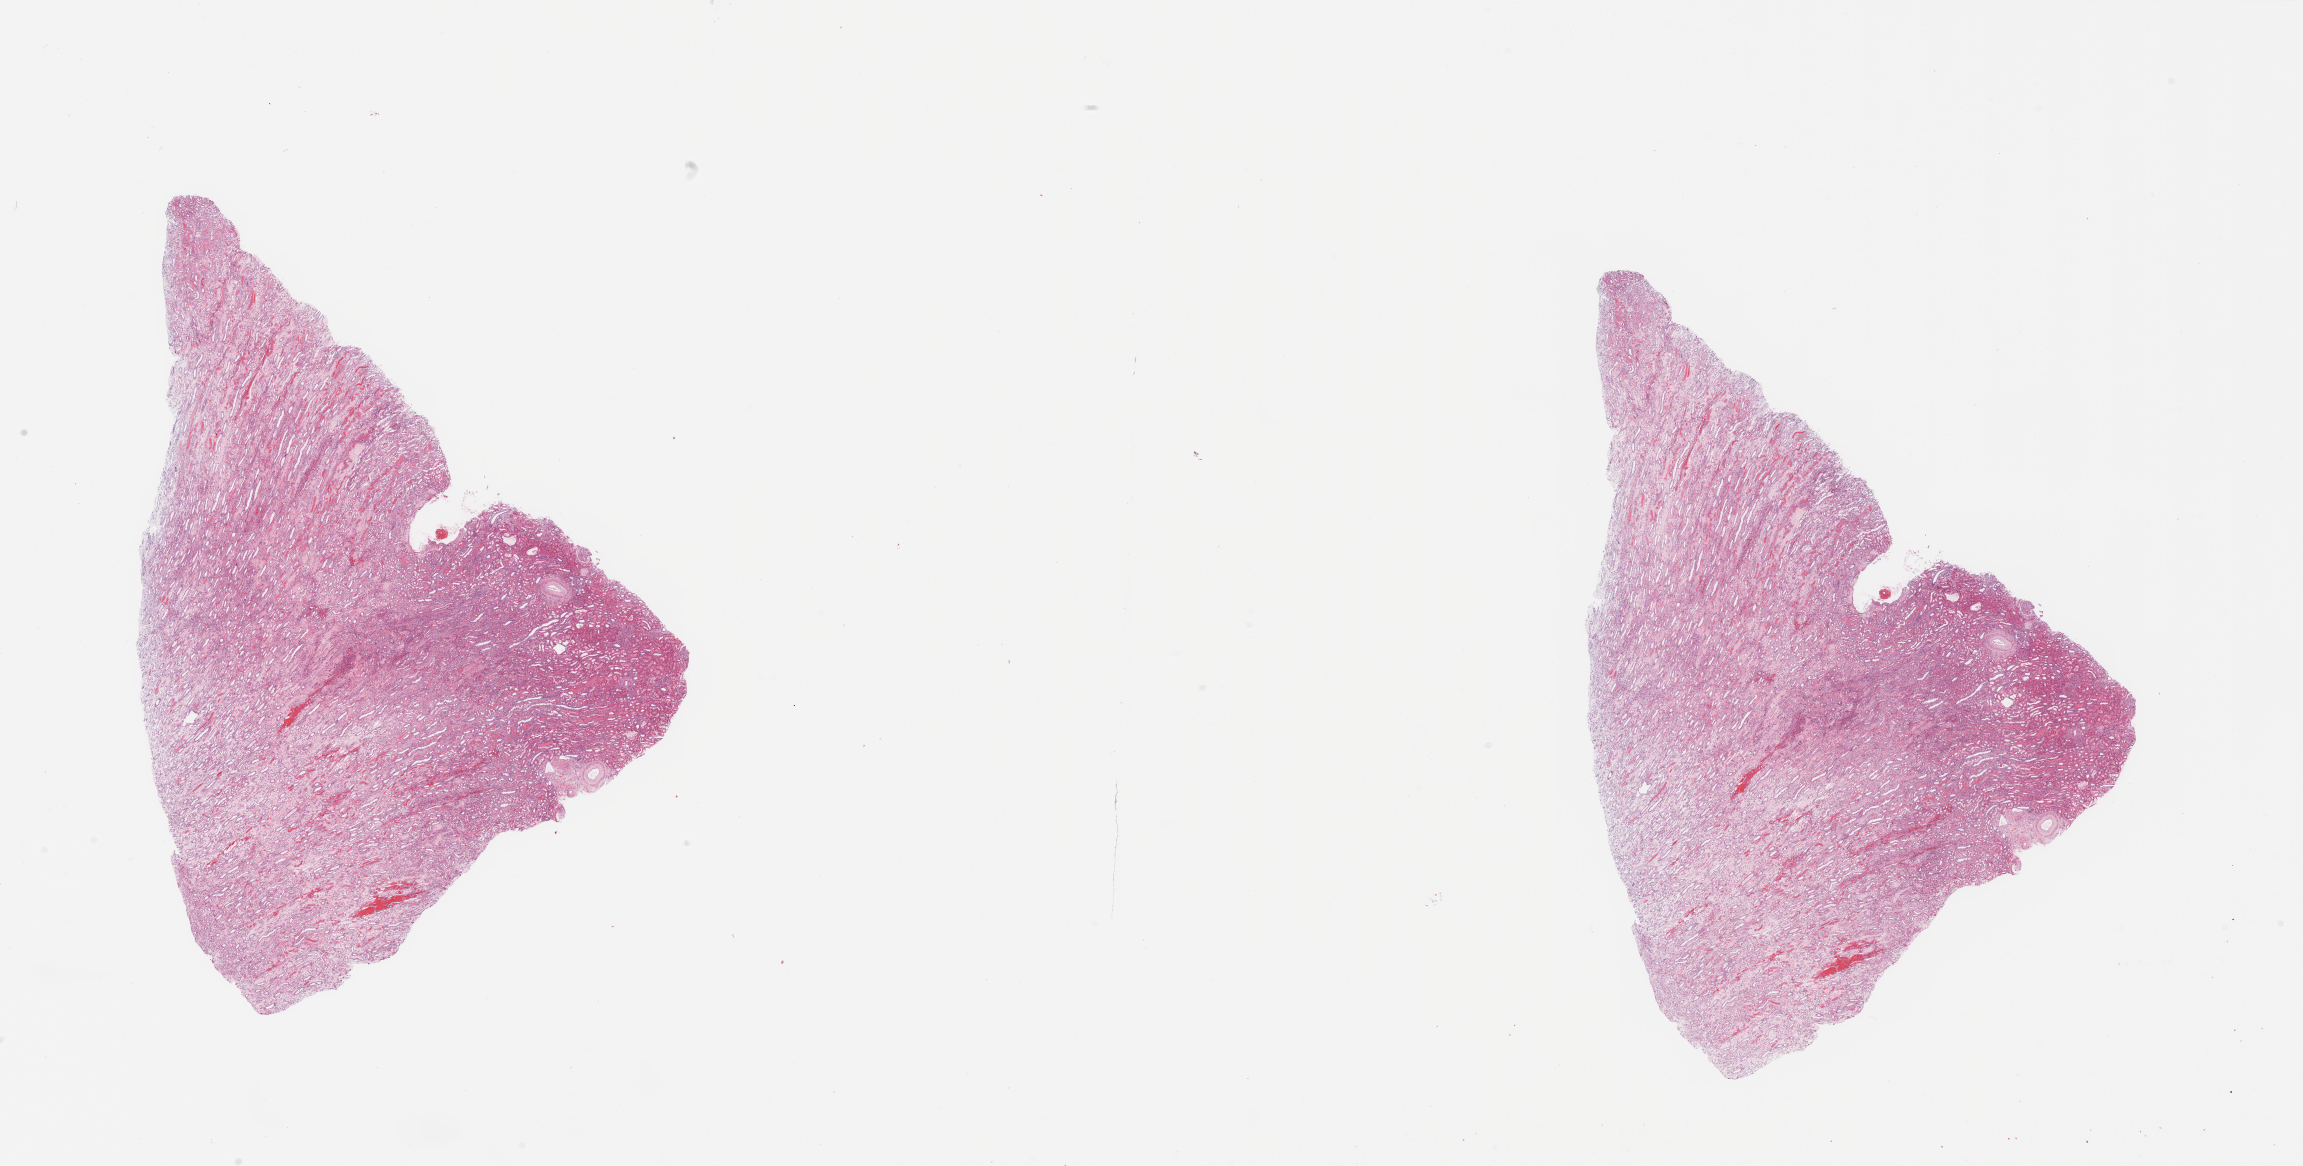
H&E whole-slide image, shown as a low-resolution overview of the whole scanned area (about 36.4 x 18.4 mm, slide scanned at 20x); normal (non-tumour) tissue sample, sampled site: kidney. Female, 72 y/o.
* this section: normal (non-tumour) tissue from the same patient
* patient diagnosis: Renal cell carcinoma, NOS